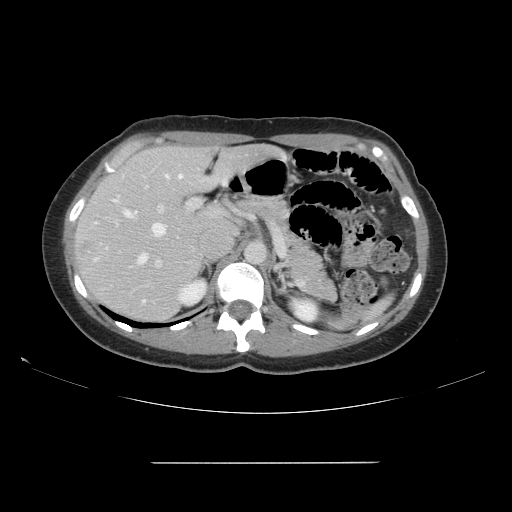
Contrast-enhanced abdominal CT, one axial slice. Position 100 of 151 along the scan axis. Soft-tissue window (W 400 / L 40 HU). 512 × 512 image matrix, field of view 421 × 421 mm. Female patient, age 46 years. From the clinical record (not read from this slice): diagnosis: colorectal cancer liver metastases, imaged before liver resection; multiple liver metastases: yes; largest metastasis: 3 cm.
Structures marked on this image (expert manual segmentation):
- hepatic veins: bounding box <95,174,183,264> (left, top, right, bottom; pixels)
- liver: <74,145,273,322>
- planned liver remnant (the part of the liver to remain after resection): <89,148,275,255>
- portal vein (with intrahepatic branches): <115,176,201,303>
- liver metastasis: <82,245,89,250>